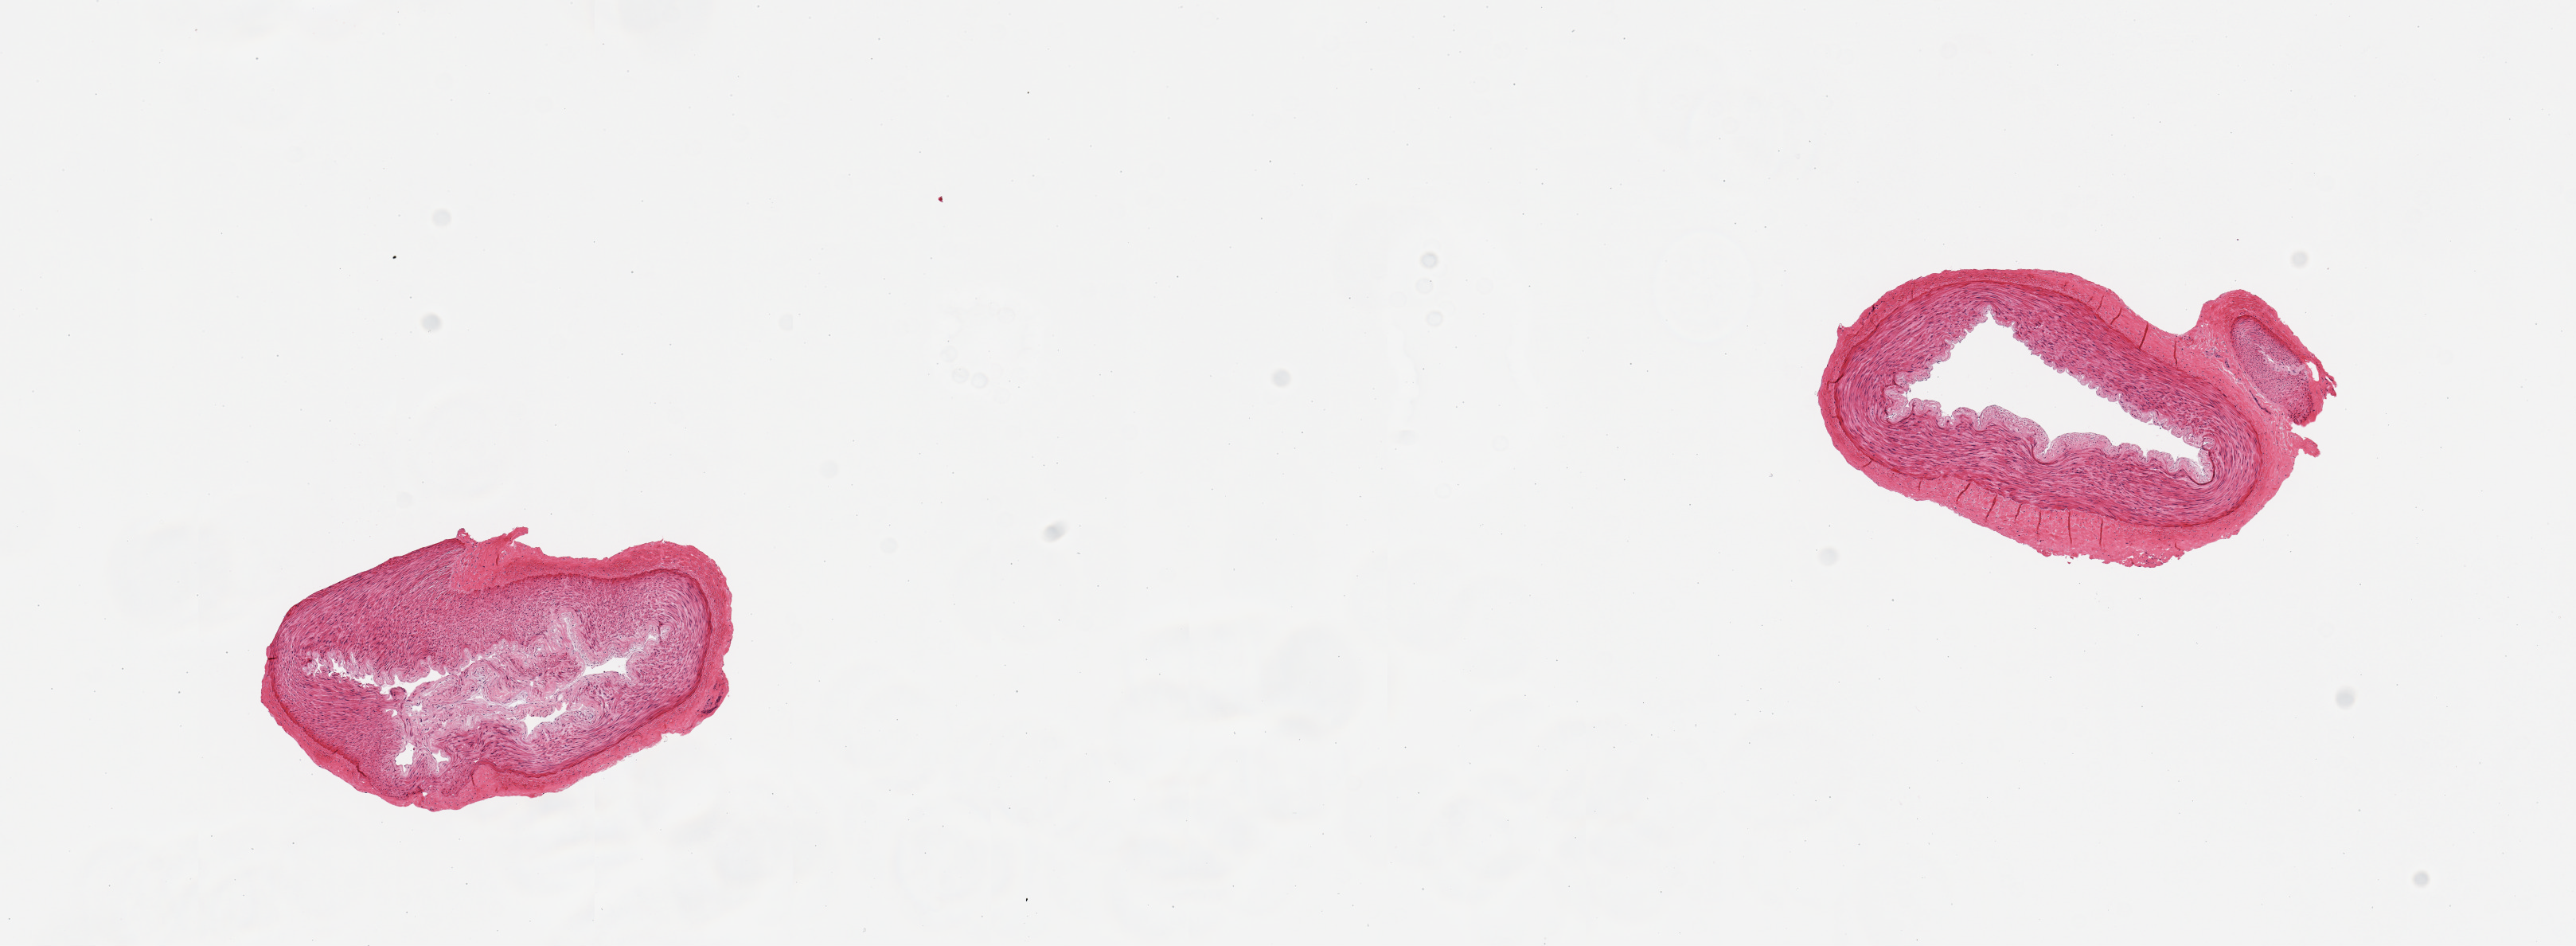
Whole-slide image, haematoxylin and eosin stain — low-resolution overview of the scanned area, about 12.8 x 4.7 mm (slide scanned at 20x); PAXgene-fixed paraffin-embedded (PFPE) section; target tissue: tibial artery; tissue donor sample. Male donor.
Reviewer comment on this tissue sample: 2 pieces; focal minimal intimal thickening.